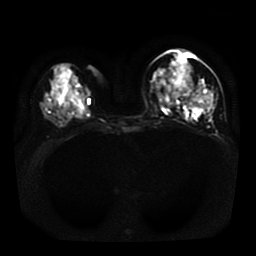
Breast MRI, one axial slice. Slice 18 of 41 in the series (ordered by position). Diffusion-weighted series; image 2 of 4 stored at this slice position (different b-values; order by instance number). 1.5 T. 5 mm slice thickness. 256 × 256 image matrix, field of view 330 × 330 mm. Female patient.
Outlined on this slice (expert manual segmentation):
- tumour on diffusion-weighted imaging: bounding box [x1, y1, x2, y2] px = [172, 92, 210, 108]